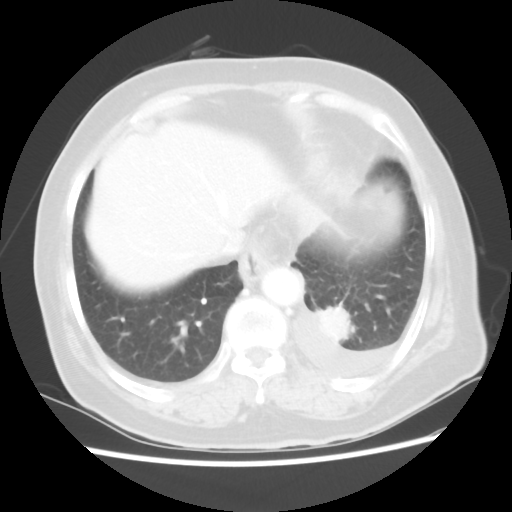
Chest CT, one axial slice. Position 12 of 80 along the scan axis. Reconstruction kernel STANDARD. 100 kVp. Lung window (W 1500 / L -600 HU). 5 mm slice thickness. 512 × 512 image matrix, field of view 343 × 343 mm. Patient: female, 68 years. From the clinical record (not read from this slice): clinical TNM (as recorded): T1c N0 M1.
Annotated regions visible in this slice (rectangle marked by the reading radiologist):
- lung tumour (recorded histology: adenocarcinoma): bounding box [x1, y1, x2, y2] px = [315, 299, 359, 346]